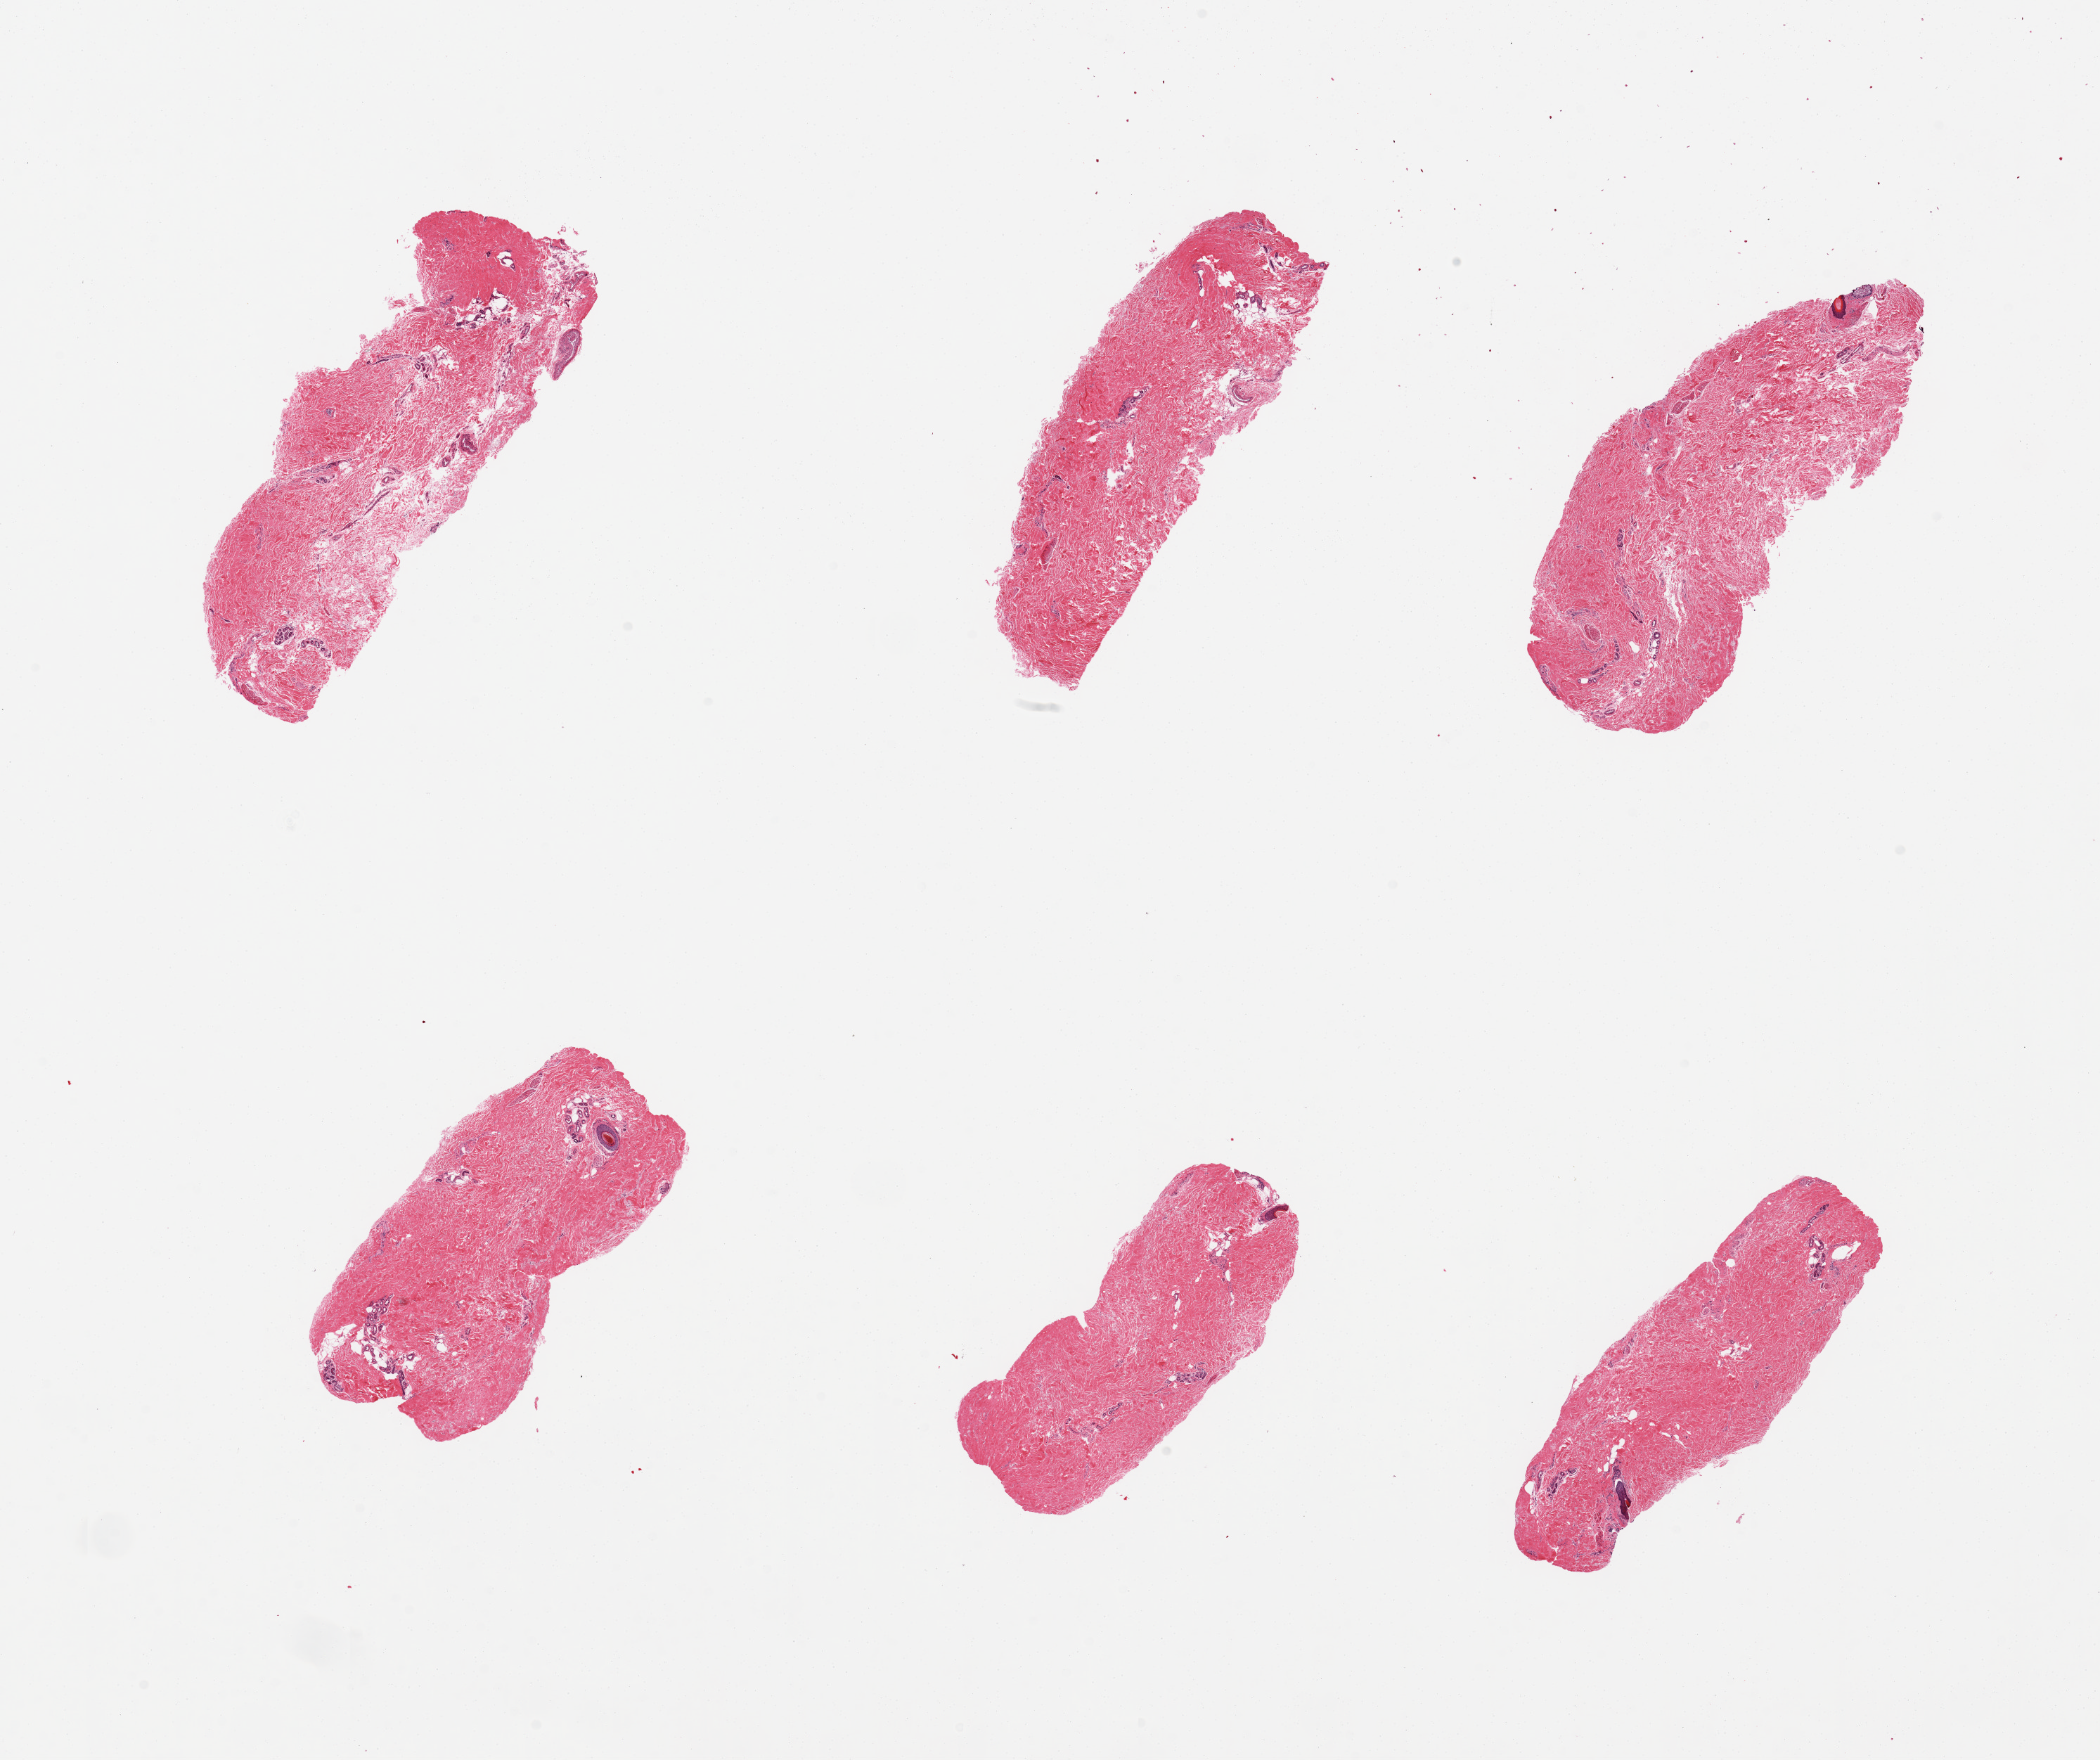
Whole-slide image, hematoxylin and eosin (H&E) stain, brightfield, a low-resolution overview of the entire scanned area, about 23.6 x 19.8 mm (acquisition: 20x scan), PAXgene-fixed paraffin-embedded (PFPE) section, sampled site (target tissue): skin of lower leg, tissue donor sample.
Pathologist's review note for this sample: 6 pieces; all dermis, no epidermis; may have been incorrectly embedded.